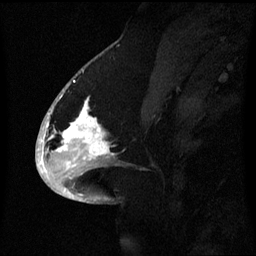
Breast MRI (dynamic contrast-enhanced), one sagittal slice. Slice 30 of 60 in the series (ordered by position). Dynamic contrast-enhanced series, image 2 of 3 at this slice position (ordered by acquisition). 1.5 T. TE 4.2 ms, TR 8.4 ms. 256 × 256 image matrix, field of view 220 × 220 mm. Patient: female, 53 years. Case-level facts recorded for this patient, not image findings: setting: breast cancer imaged before/during neoadjuvant chemotherapy; receptor status: HR-positive, HER2-negative.
Outlined on this slice (semi-automatic segmentation, software-assisted and operator-edited):
- analysis volume of interest (the breast-tissue region the enhancement analysis was run in; not a lesion): bounding box <52,90,120,171> (left, top, right, bottom; pixels)
- tumour enhancement mask (voxels above the 70 % enhancement threshold inside the analysis volume of interest): <53,98,111,159>